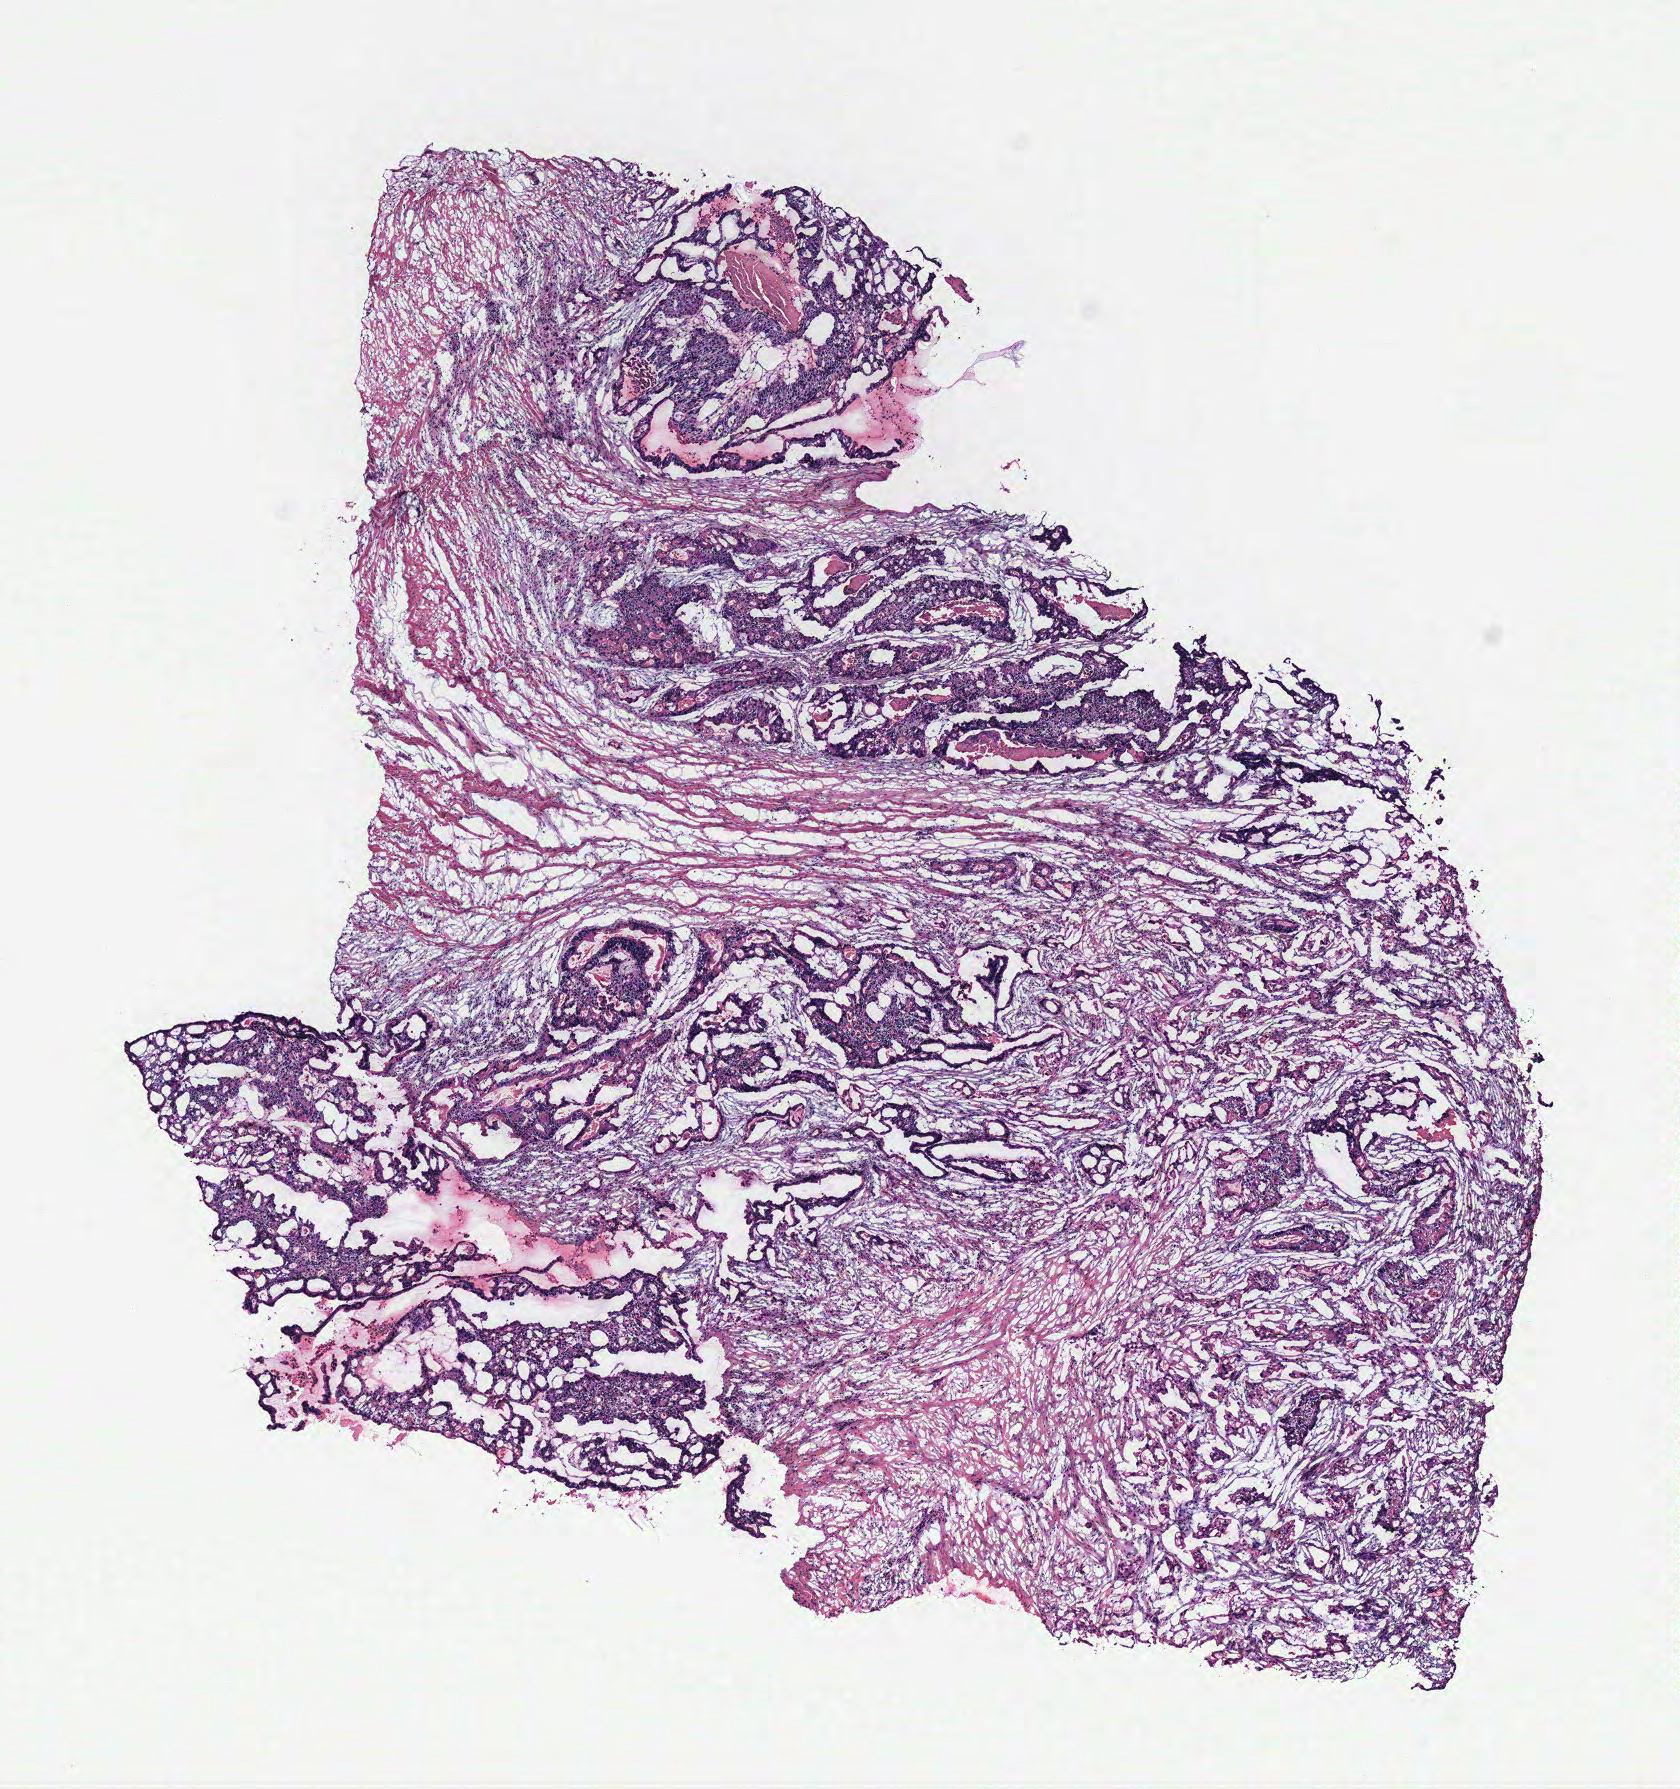
H&E whole-slide image, whole scanned area (about 6.7 x 7.2 mm, slide scanned at 40x) shown as a low-resolution overview. Colon, tumour tissue. Female, 54 y/o.
Primary tumour site (as recorded): colon. Histologic diagnosis: Adenocarcinoma, NOS. AJCC pathologic stage: IIIB.